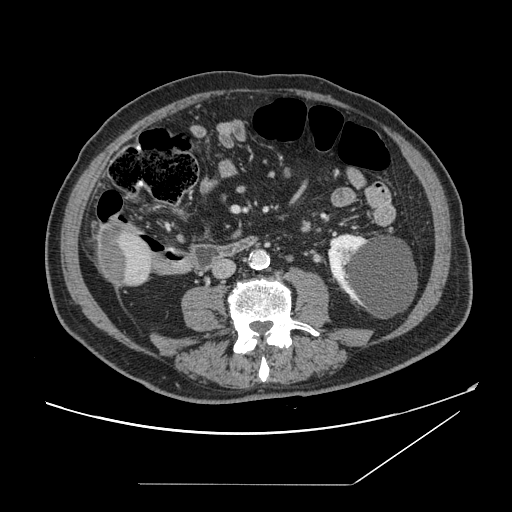
Contrast-enhanced abdominal CT, one axial slice; slice 28 of 166 in the series (ordered by position); intravenous contrast given; soft-tissue window (W 400 / L 40 HU); 2.5 mm slice thickness; 512 × 512 image matrix, field of view 416 × 416 mm. Male patient, age 80 years. Case-level facts recorded for this patient, not image findings: diagnosis: colorectal cancer liver metastases, imaged before liver resection; multiple liver metastases: no; largest metastasis: 2.2 cm.
Outlined on this slice (outlined manually by an expert reader):
- liver: box from (x=96, y=225) to (x=154, y=288) px
- liver metastasis: (x=98, y=232)–(x=129, y=285)